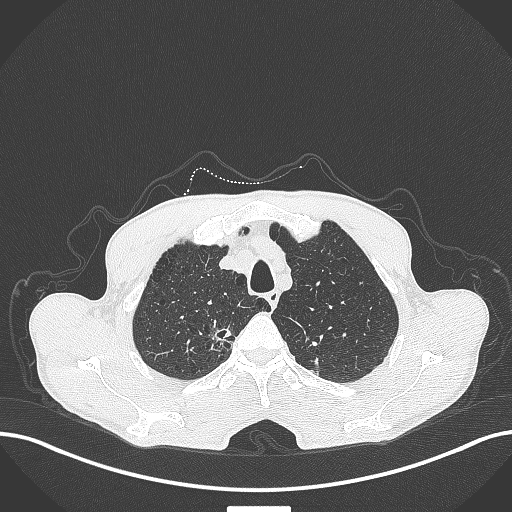
Chest CT, one axial slice. Slice 362 of 445 in the series (ordered by position). Reconstruction kernel B70f. 120 kVp. Lung window (W 1500 / L -600 HU). 1 mm slice thickness. 512 × 512 image matrix. Male patient, age 70 years. From the clinical record (not read from this slice): clinical TNM (as recorded): T1a N0 M0; histopathological grade: G1-2.
Outlined on this slice (rectangle marked by the reading radiologist):
- lung tumour (recorded histology: adenocarcinoma): bounding box [x1, y1, x2, y2] px = [210, 325, 236, 346]